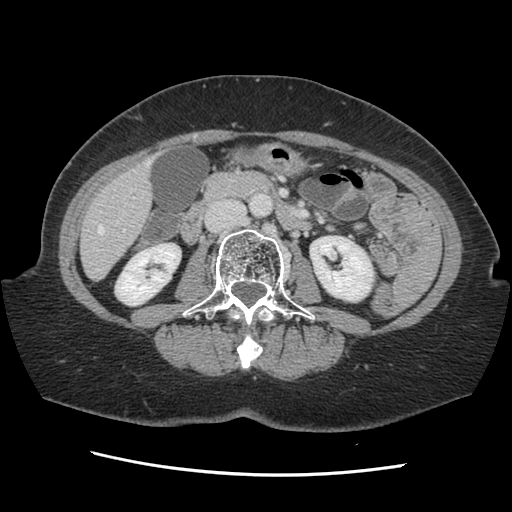
Contrast-enhanced abdominal CT, one axial slice; slice 45 of 141 in the series (ordered by position); 120 kVp; soft-tissue window (W 400 / L 40 HU); 2.5 mm slice thickness; 512 × 512 image matrix, field of view 330 × 330 mm. Female patient, age 61 years. From the clinical record (not read from this slice): diagnosis: colorectal cancer liver metastases, imaged before liver resection; multiple liver metastases: no; largest metastasis: 2.4 cm; disease in both lobes: no.
Outlined on this slice (manually delineated by an expert):
- hepatic veins: bounding box [x1, y1, x2, y2] px = [96, 161, 149, 271]
- liver: [82, 164, 153, 279]
- planned liver remnant (the part of the liver to remain after resection): [82, 180, 152, 279]